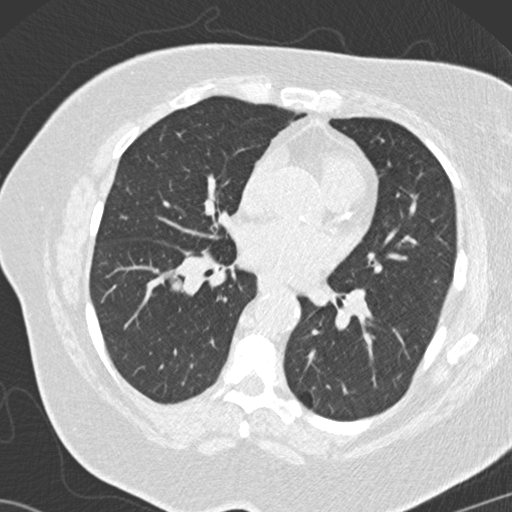
Low-dose screening chest CT, one axial slice. Slice 68 of 146 in the series (ordered by position). 120 kVp. Lung window (W 1500 / L -600 HU). 512 × 512 image matrix, field of view 350 × 350 mm.
Outlined on this slice (manually delineated by an expert):
- lesion 4 (tumor, lower lobe of right lung): bounding box [x1, y1, x2, y2] px = [168, 275, 184, 296]